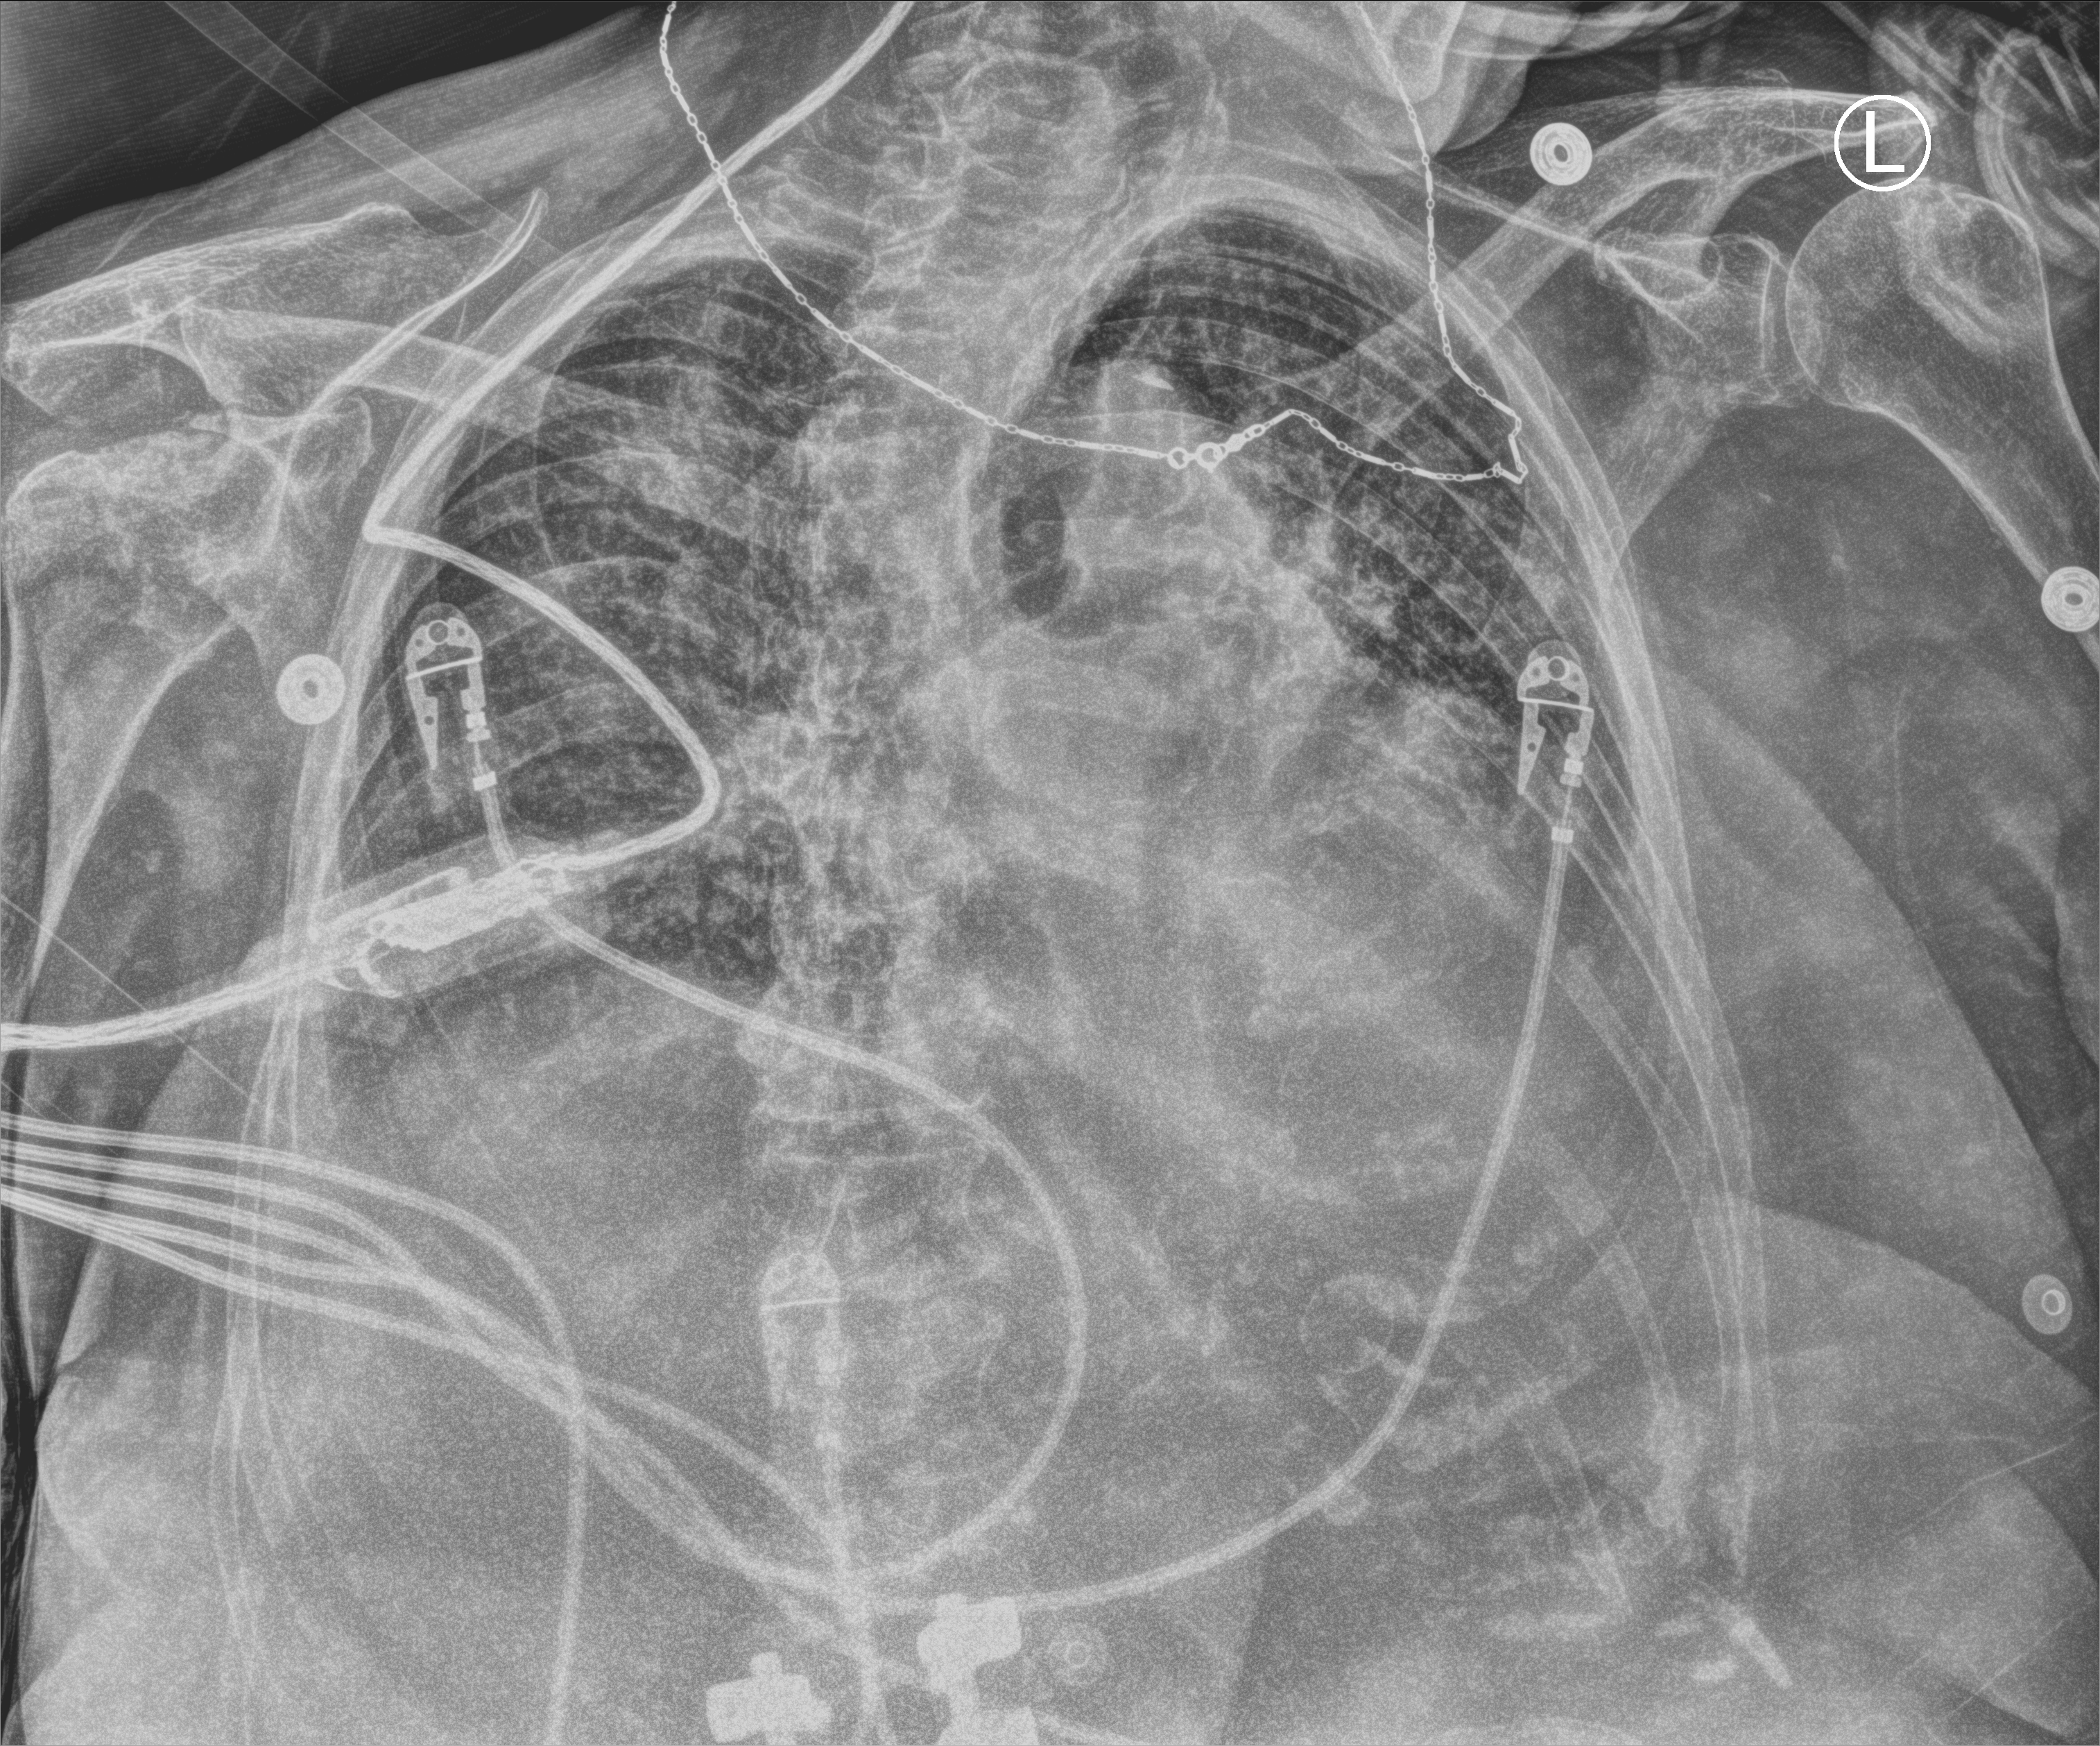
Bedside chest radiograph (computed radiography), anteroposterior (AP) projection. Female patient hospitalised with COVID-19, age 75–90 years.
Hospital-stay facts (about this admission, not read from this image; timing relative to this image not recorded):
- length of hospital stay: 5 days
- smoking status (admission record): former
- admitted to intensive care during this hospital stay: no